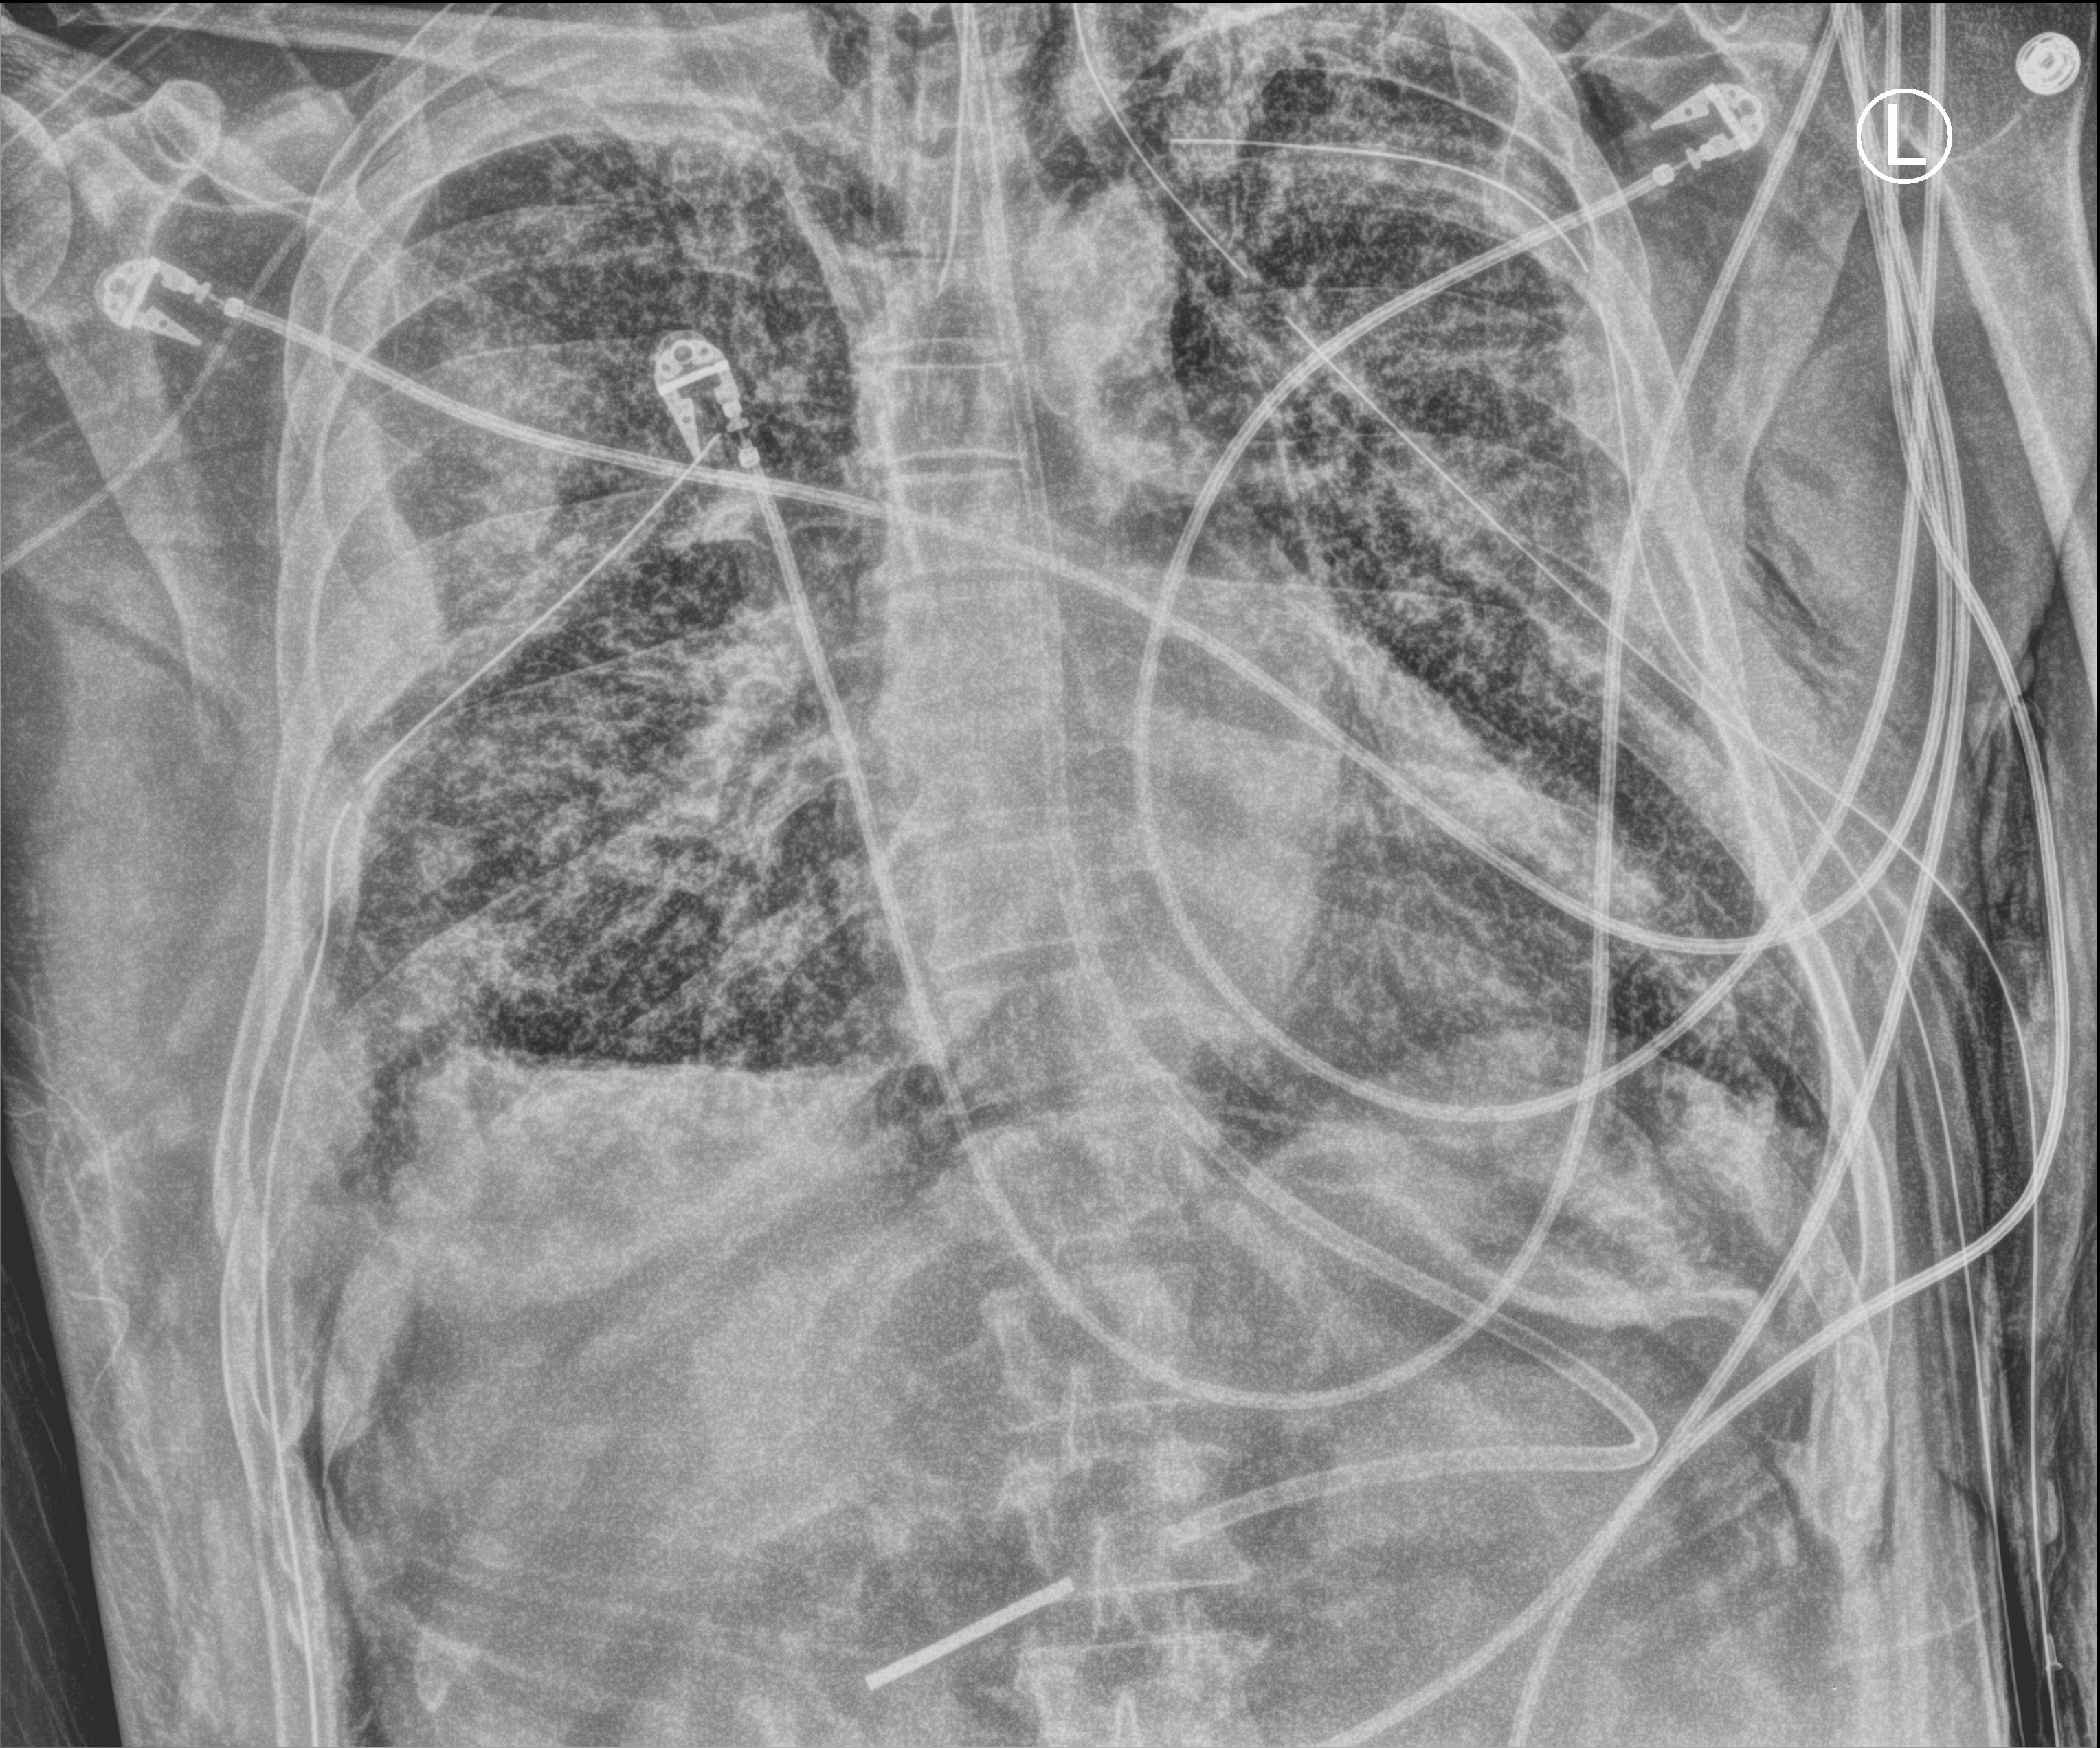
Bedside chest radiograph (computed radiography), anteroposterior (AP) projection. Male patient hospitalised with COVID-19, age 18–59 years.
Admission-level facts for this patient (not findings on this image; timing relative to this image not recorded): admitted to intensive care during this hospital stay: yes.